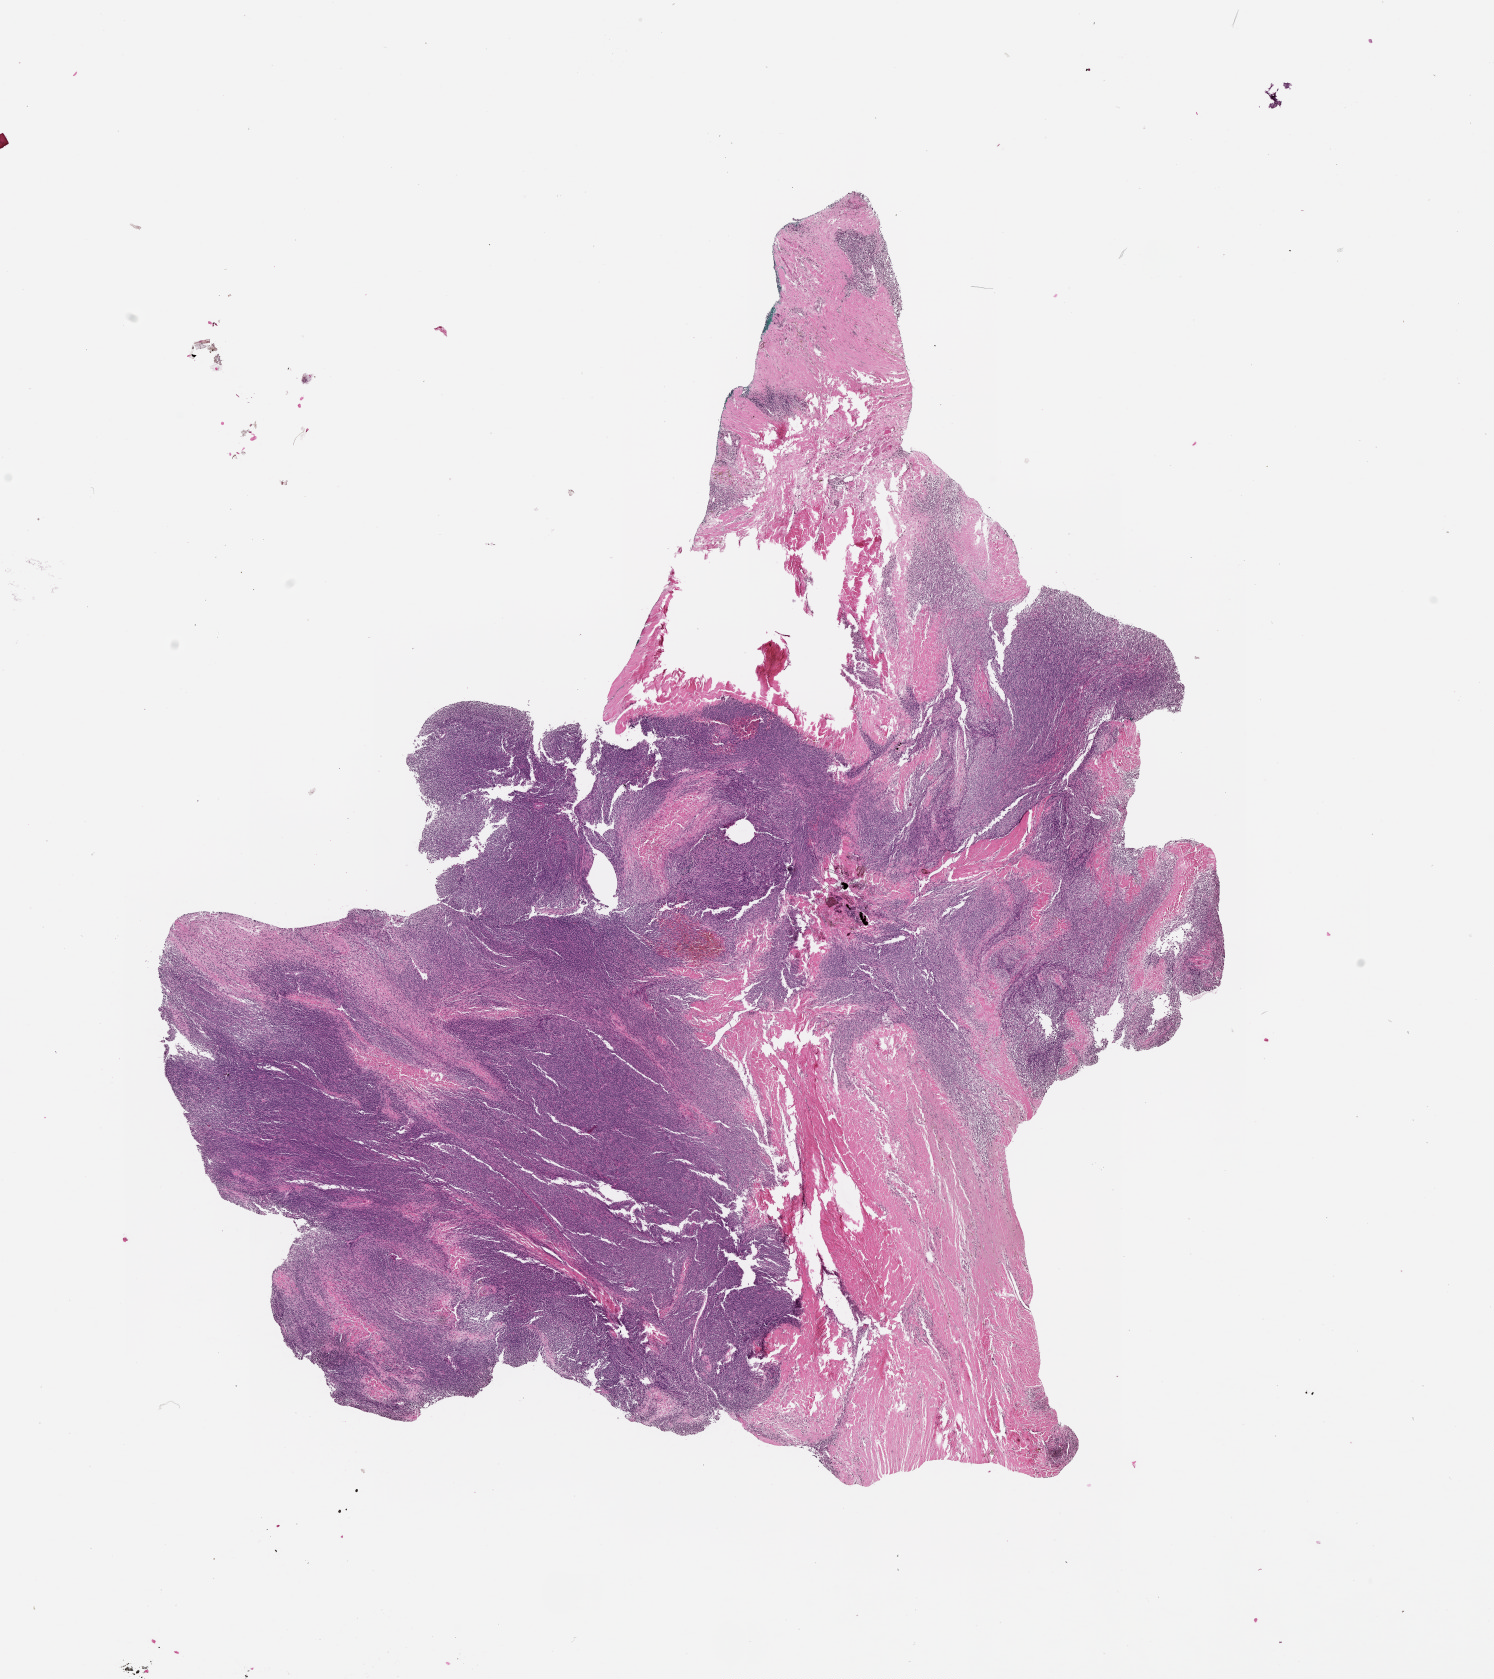
H&E-stained whole-slide image, a low-resolution overview of the entire scanned area, about 12.0 x 13.5 mm.
• patient diagnosis (cohort enrolment): sarcoma (site not recorded at cohort level)